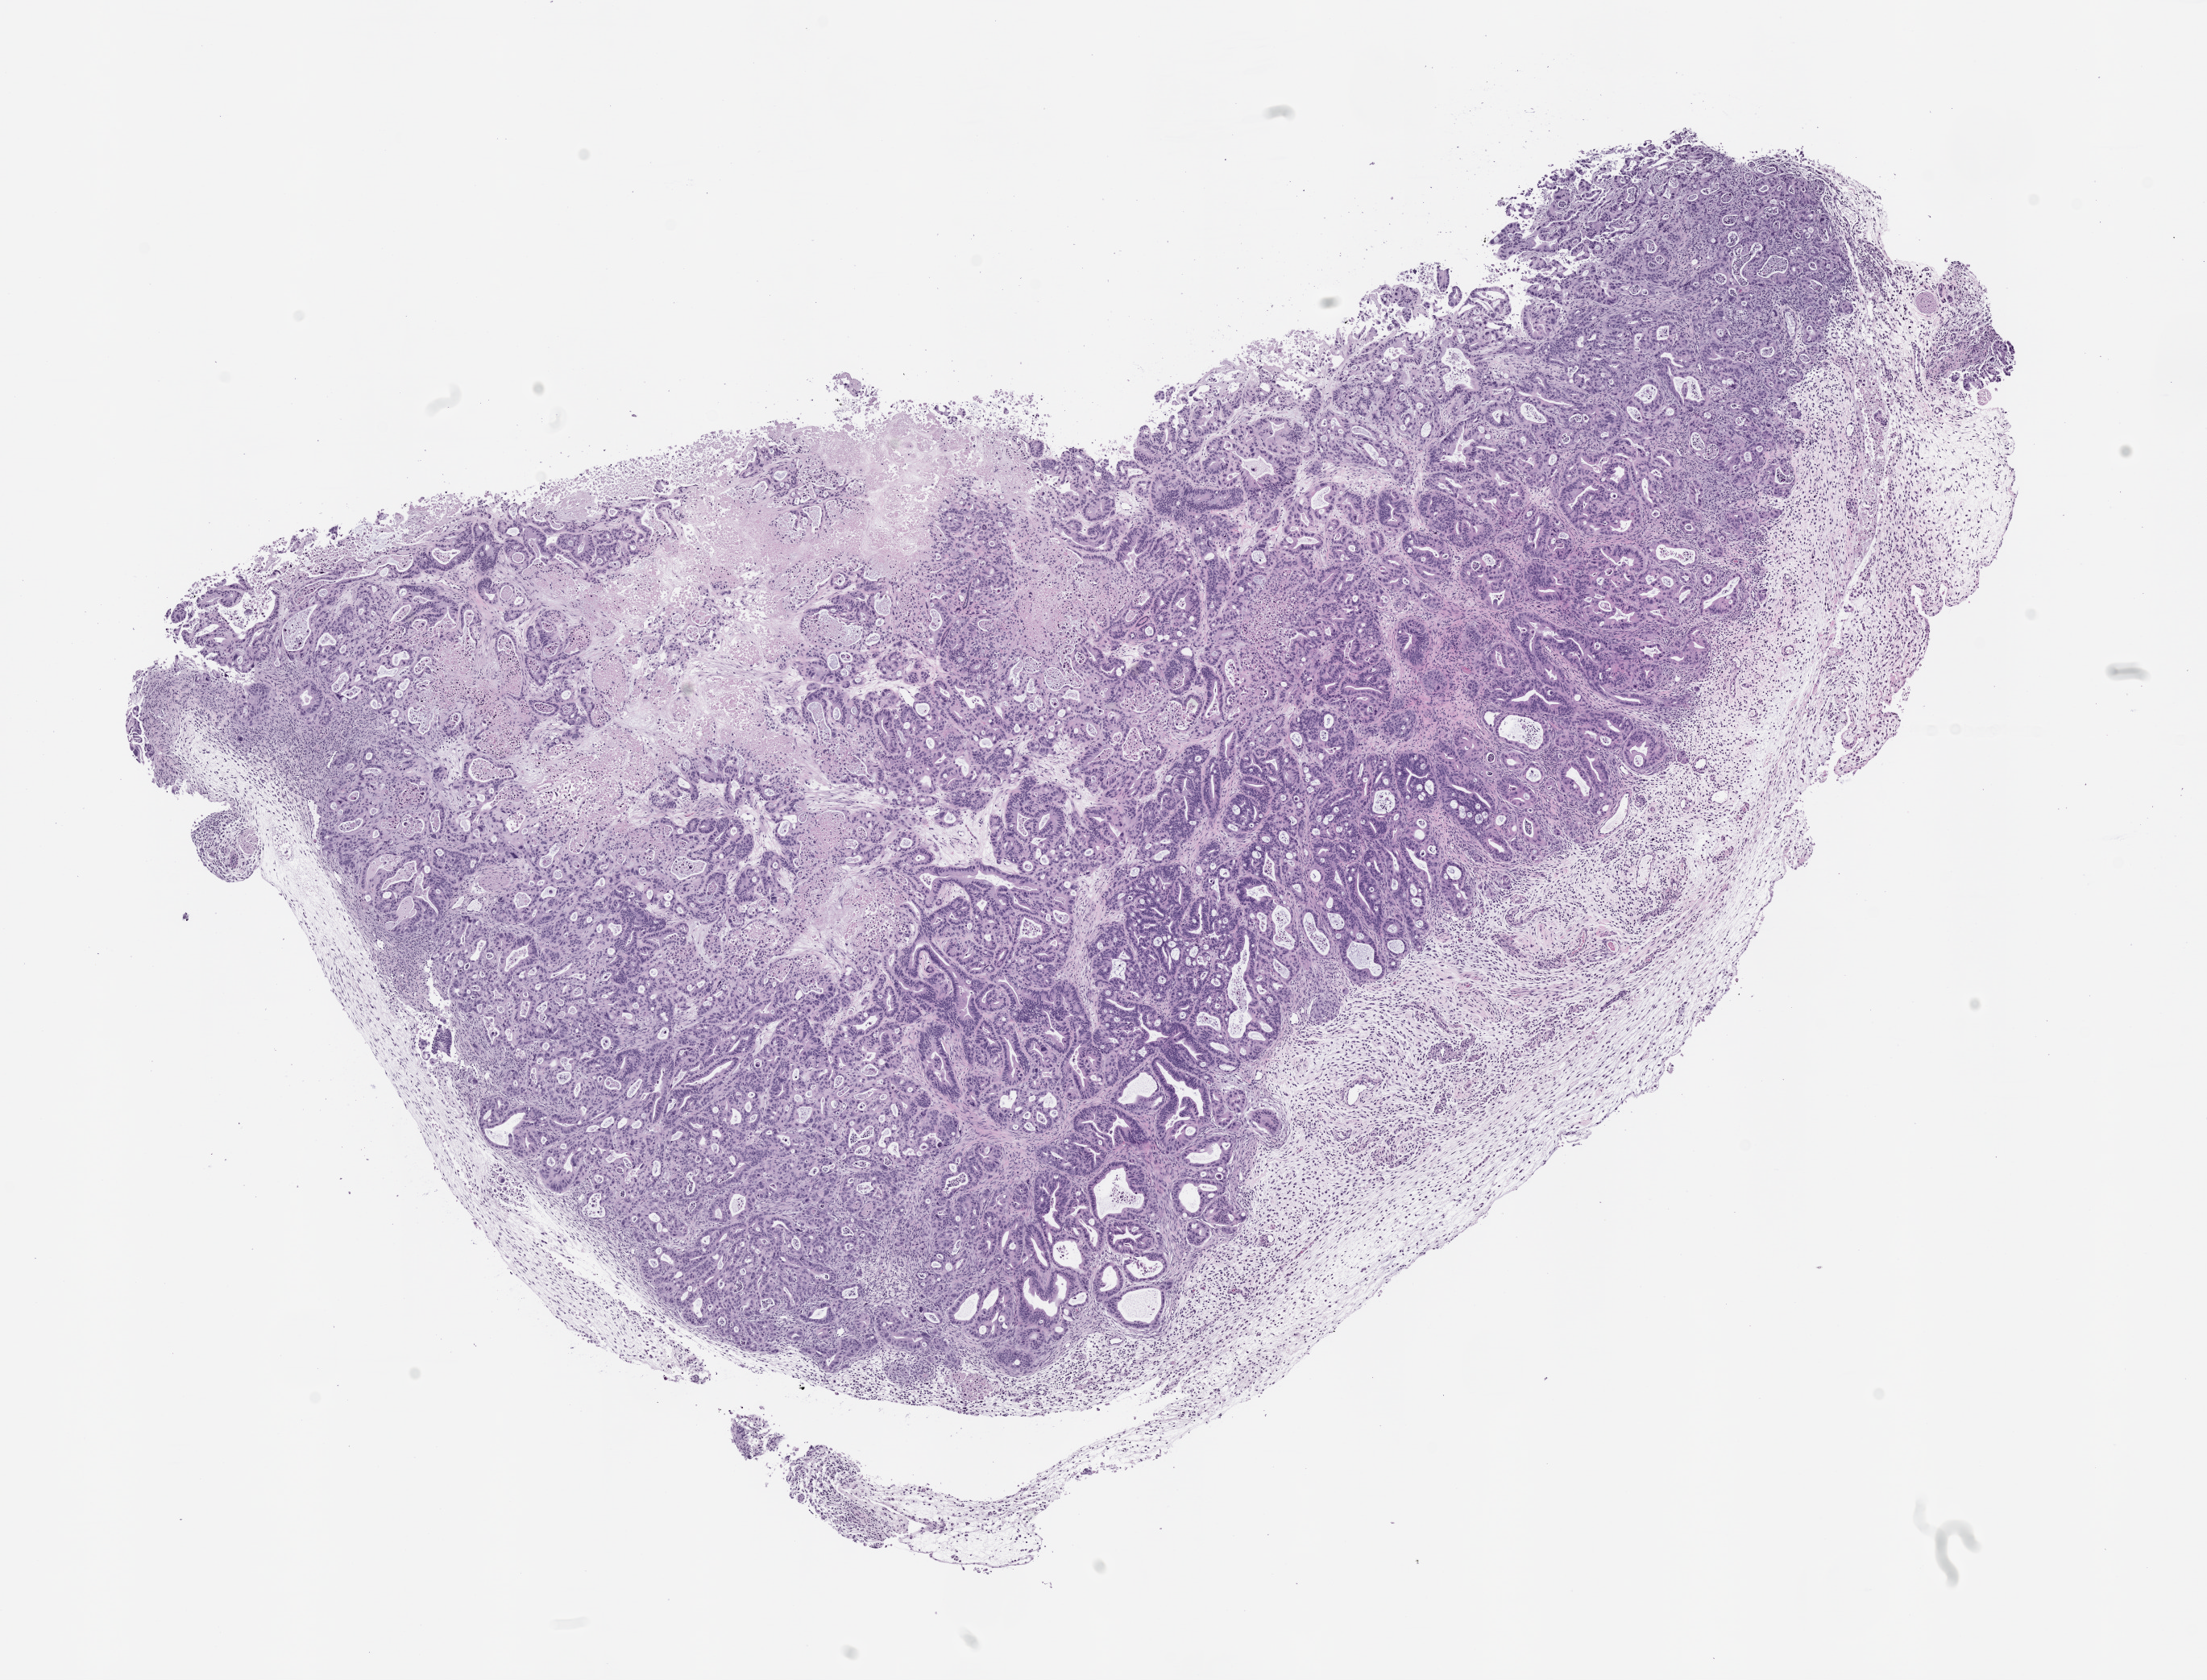
H&E whole-slide image of a patient-derived xenograft (PDX) tumor grown in a mouse, passage 0 — whole scanned area (about 11.0 x 8.4 mm) shown as a low-resolution overview; formalin-fixed, paraffin-embedded (FFPE) tissue; originating tumor site category: pancreas.
- originating patient diagnosis: Pancreatic Adenocarcinoma